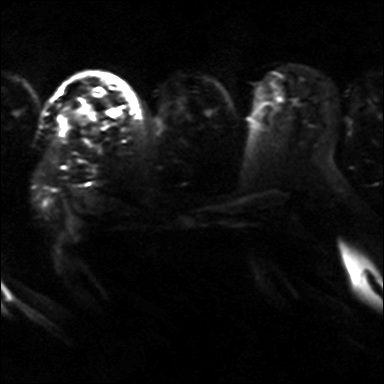
Breast MRI, one axial slice; slice 25 of 36 in the series (ordered by position); diffusion-weighted series; image 2 of 4 stored at this slice position (different b-values; order by instance number); 3 T; 384 × 384 image matrix. Female patient.
Structures marked on this image (expert manual segmentation):
- tumour on diffusion-weighted imaging: bounding box [x1, y1, x2, y2] px = [64, 105, 96, 122]